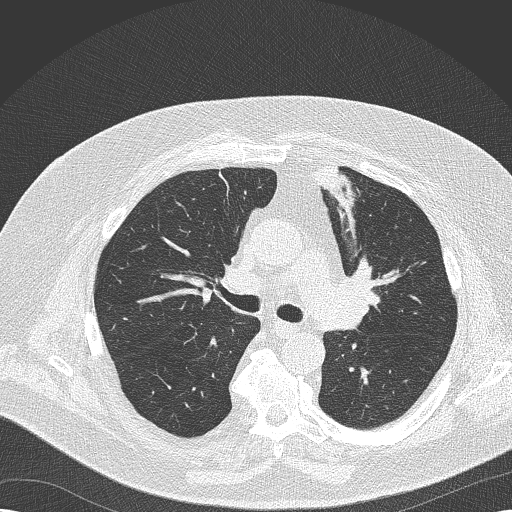
Low-dose screening chest CT, axial slice, second screening round (one year after baseline), lung window (W 1500 / L -600 HU), slice 68 of 173 in the series, 512 × 512 image matrix, field of view 370 × 370 mm. Male, age 68 years at enrolment. Former smoker at enrolment.
• Expert-annotated lung lesion, bounding box <321,265,380,328> (left, top, right, bottom; pixels).
• Screening reader's record for this exam (one nodule recorded; not confirmed to be the boxed lesion): non-calcified nodule or mass ≥4 mm, left lower lobe, 8 × 6 mm, soft tissue attenuation, pre-existing on the prior screen: yes; interval growth: no.
• Official screen result: positive, no significant change: stable abnormalities potentially related to lung cancer, unchanged since the prior screening exam.
• Later outcome: lung cancer diagnosed 256 days after this screen — squamous cell carcinoma, NOS, left upper lobe, poorly differentiated (G3), stage IIB (AJCC 6th edition), 35 mm at pathology.